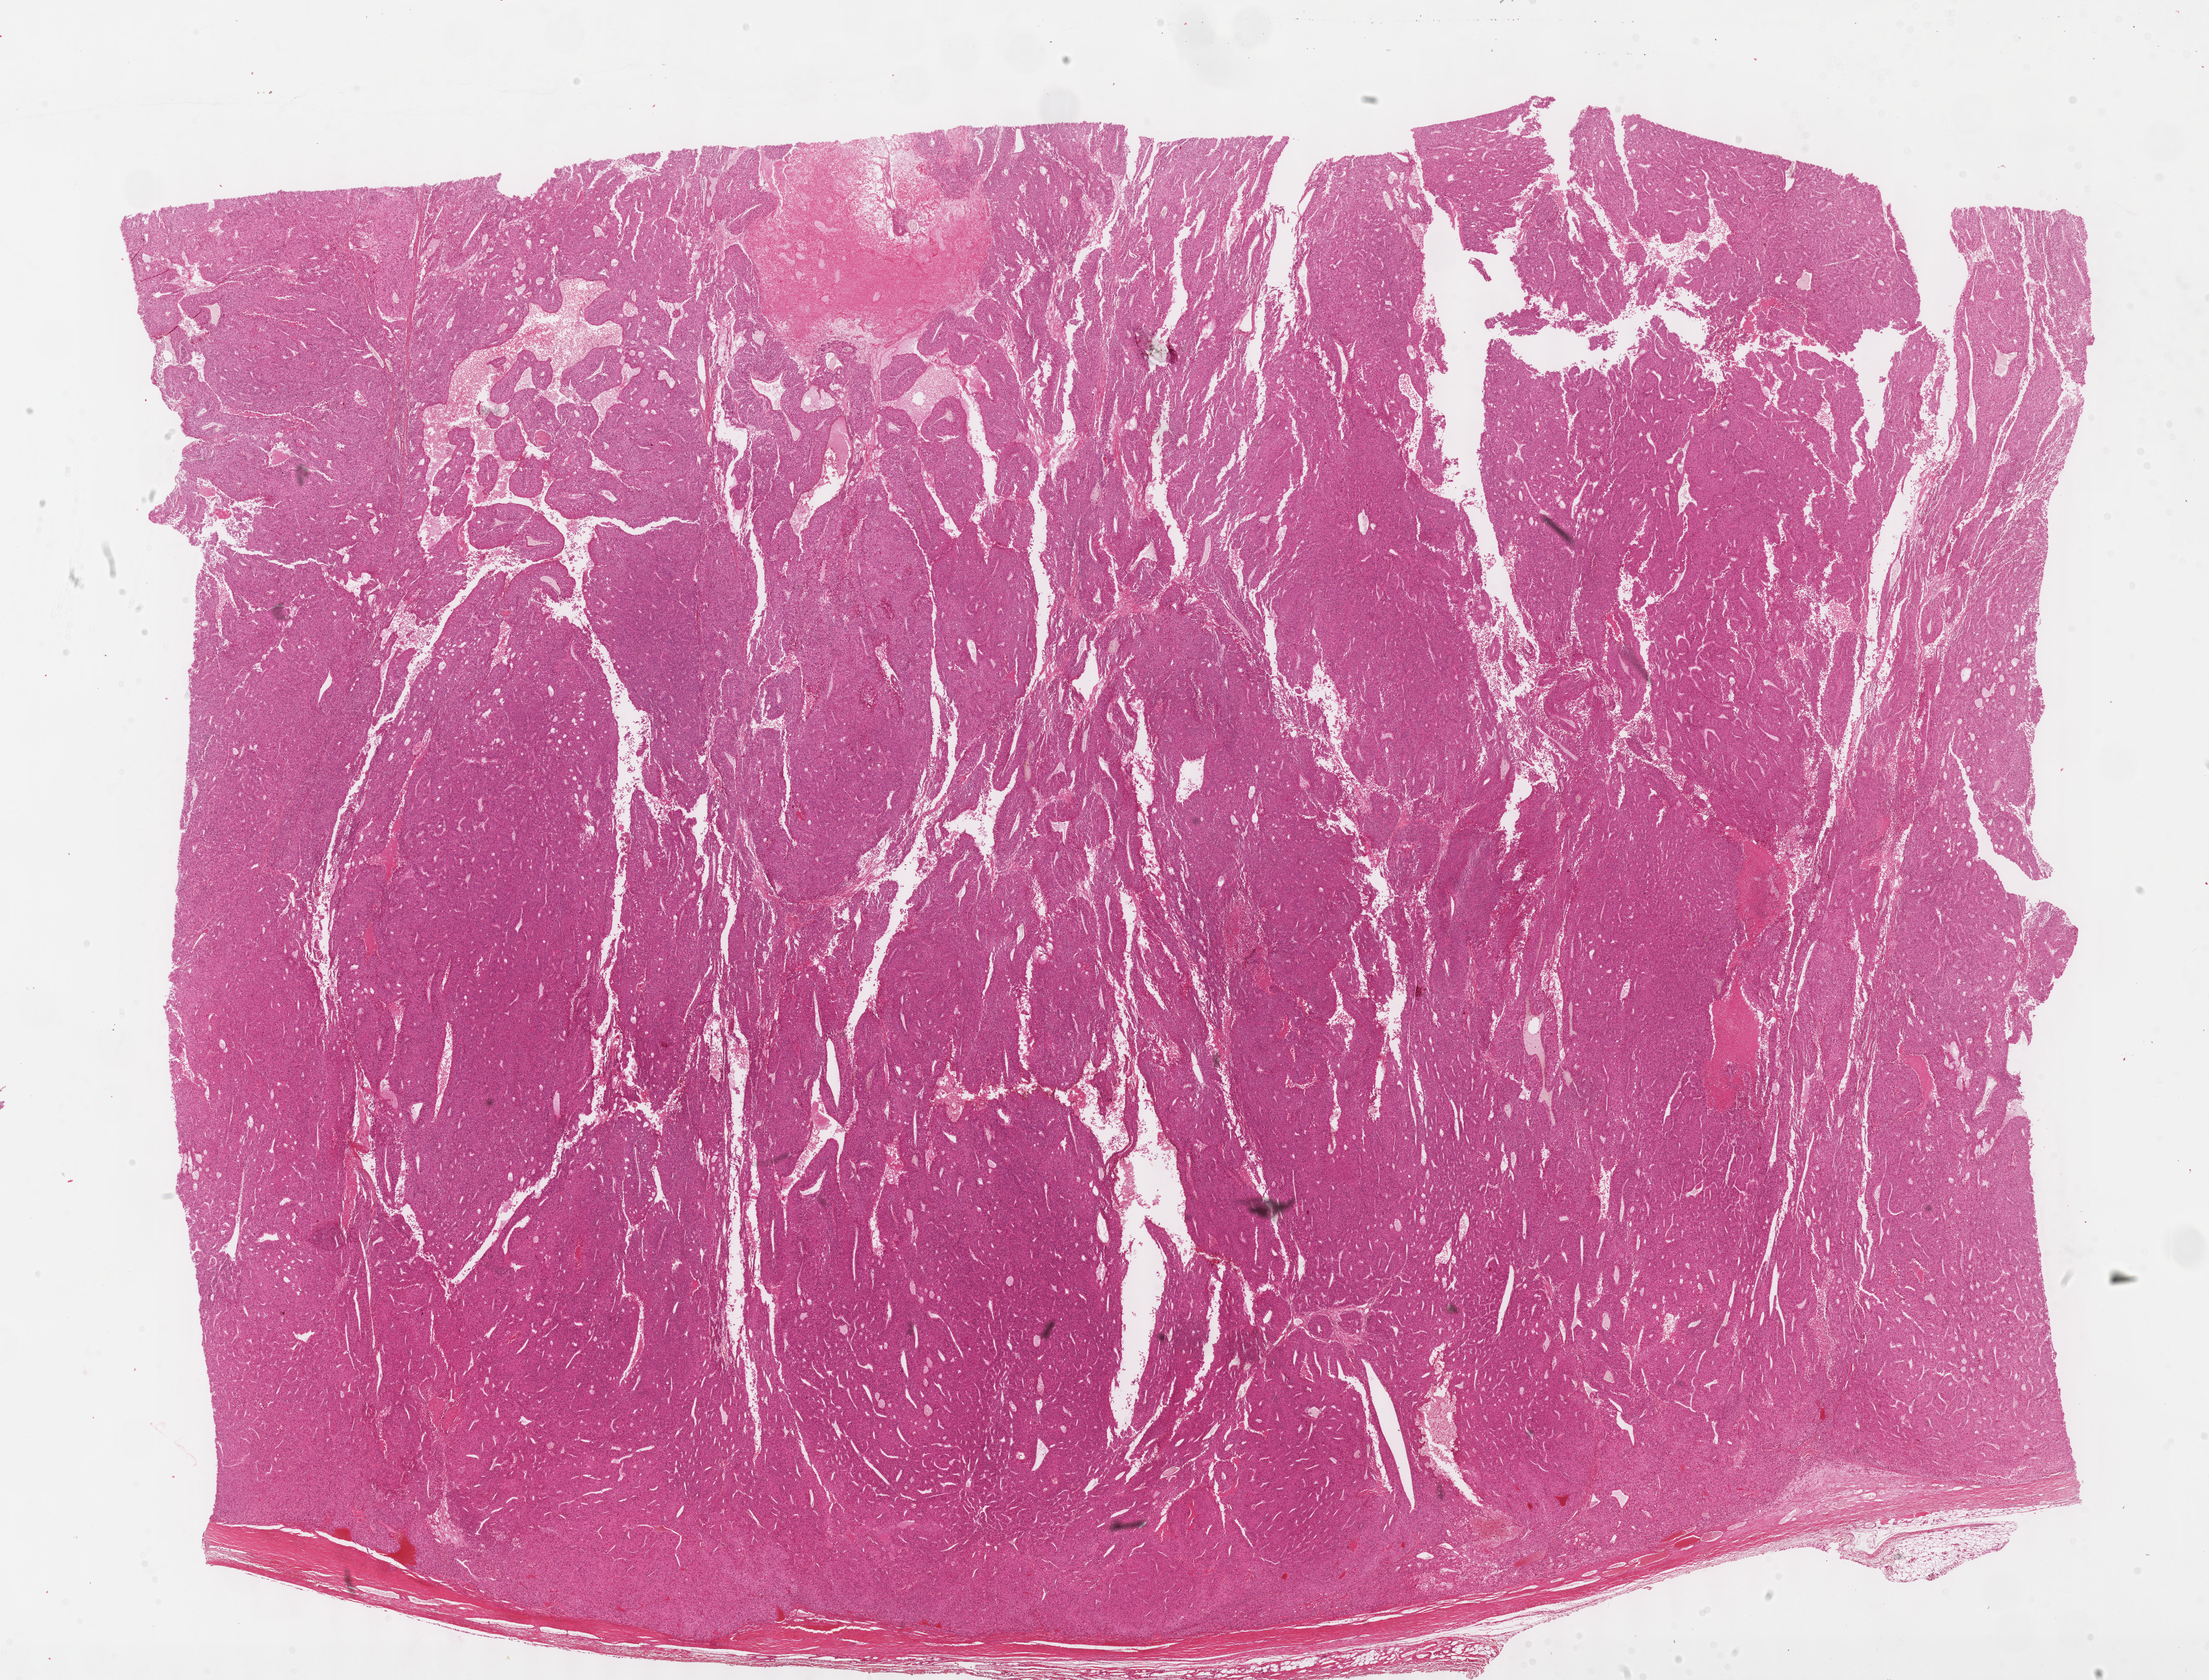
Hematoxylin and eosin (H&E) stained whole-slide image, a low-resolution overview of the entire scanned area, about 28.2 x 21.4 mm (from a 40x scan). FFPE section. Primary tumour sample from the adrenal cortex. Patient: female, age at initial diagnosis 61 years.
Pathologic diagnosis: Adrenal cortical carcinoma (cortex of adrenal gland). Laterality: right.